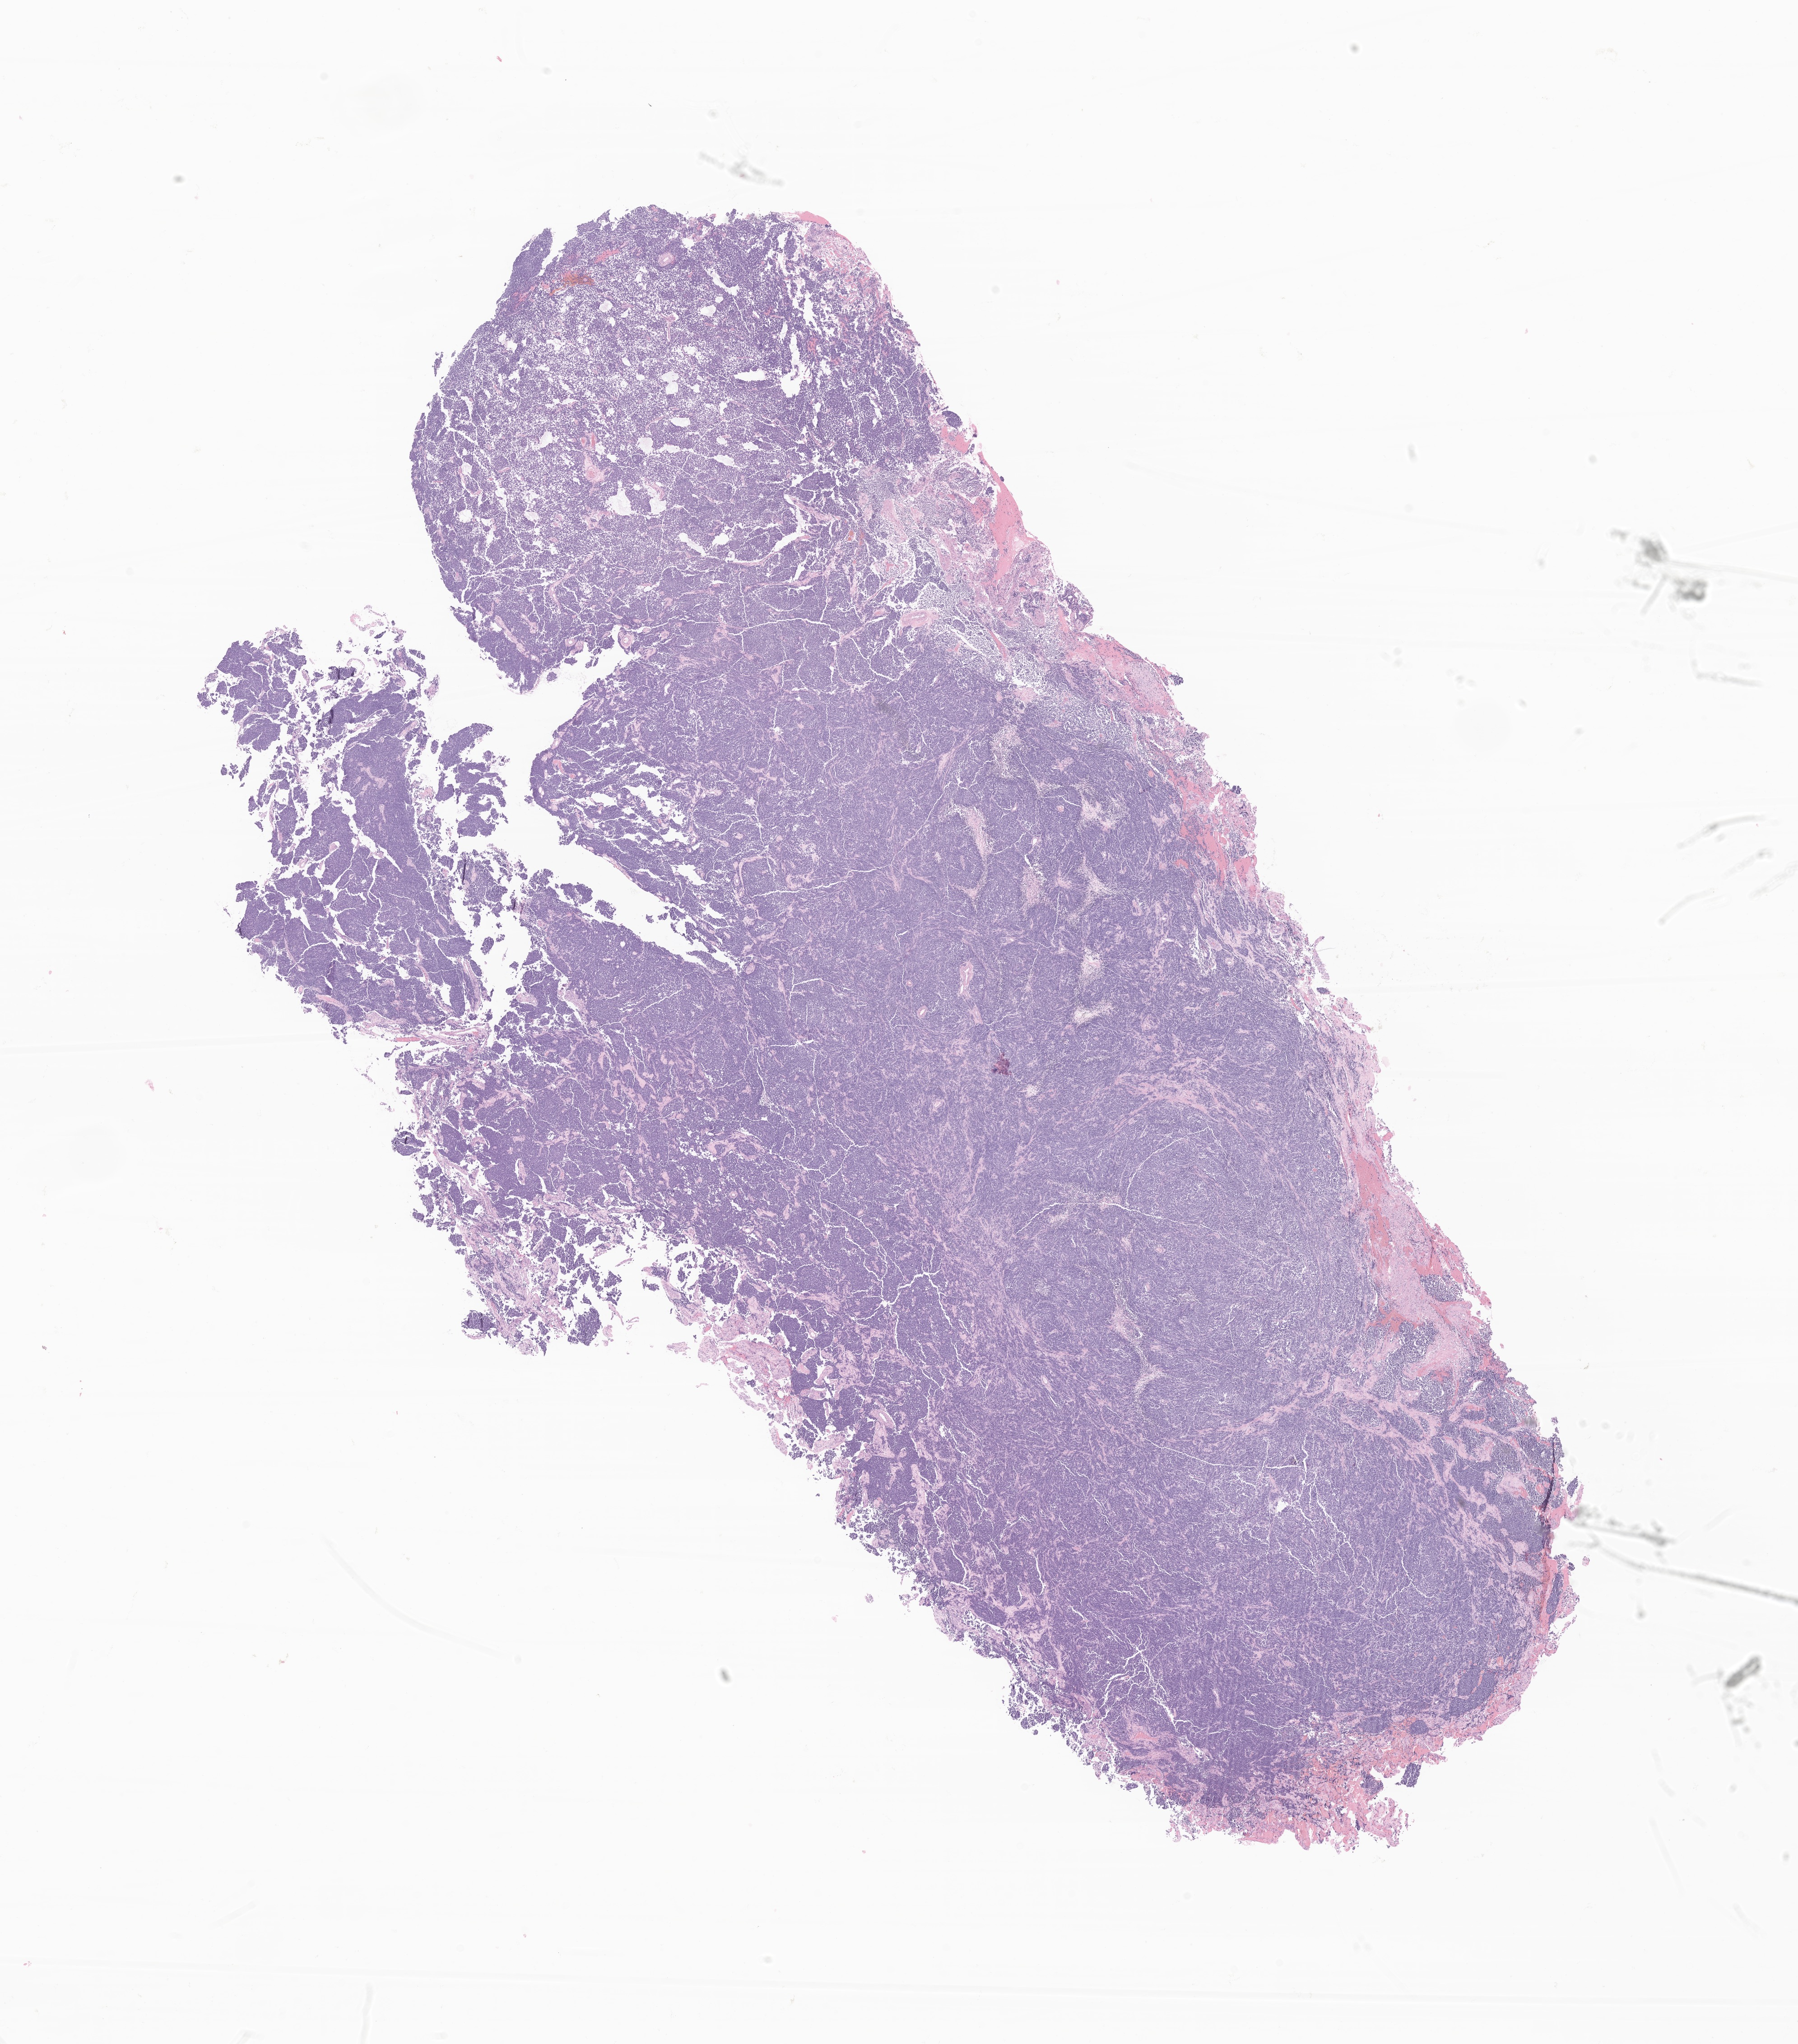
Hematoxylin and eosin (H&E) whole-slide image of tumor tissue from the brain, shown as a low-resolution overview of the whole scanned area (about 16.8 x 19.1 mm). Formalin-fixed, paraffin-embedded (FFPE) tissue. Male patient, age 48 months.
* diagnosis: Neoplasm, malignant